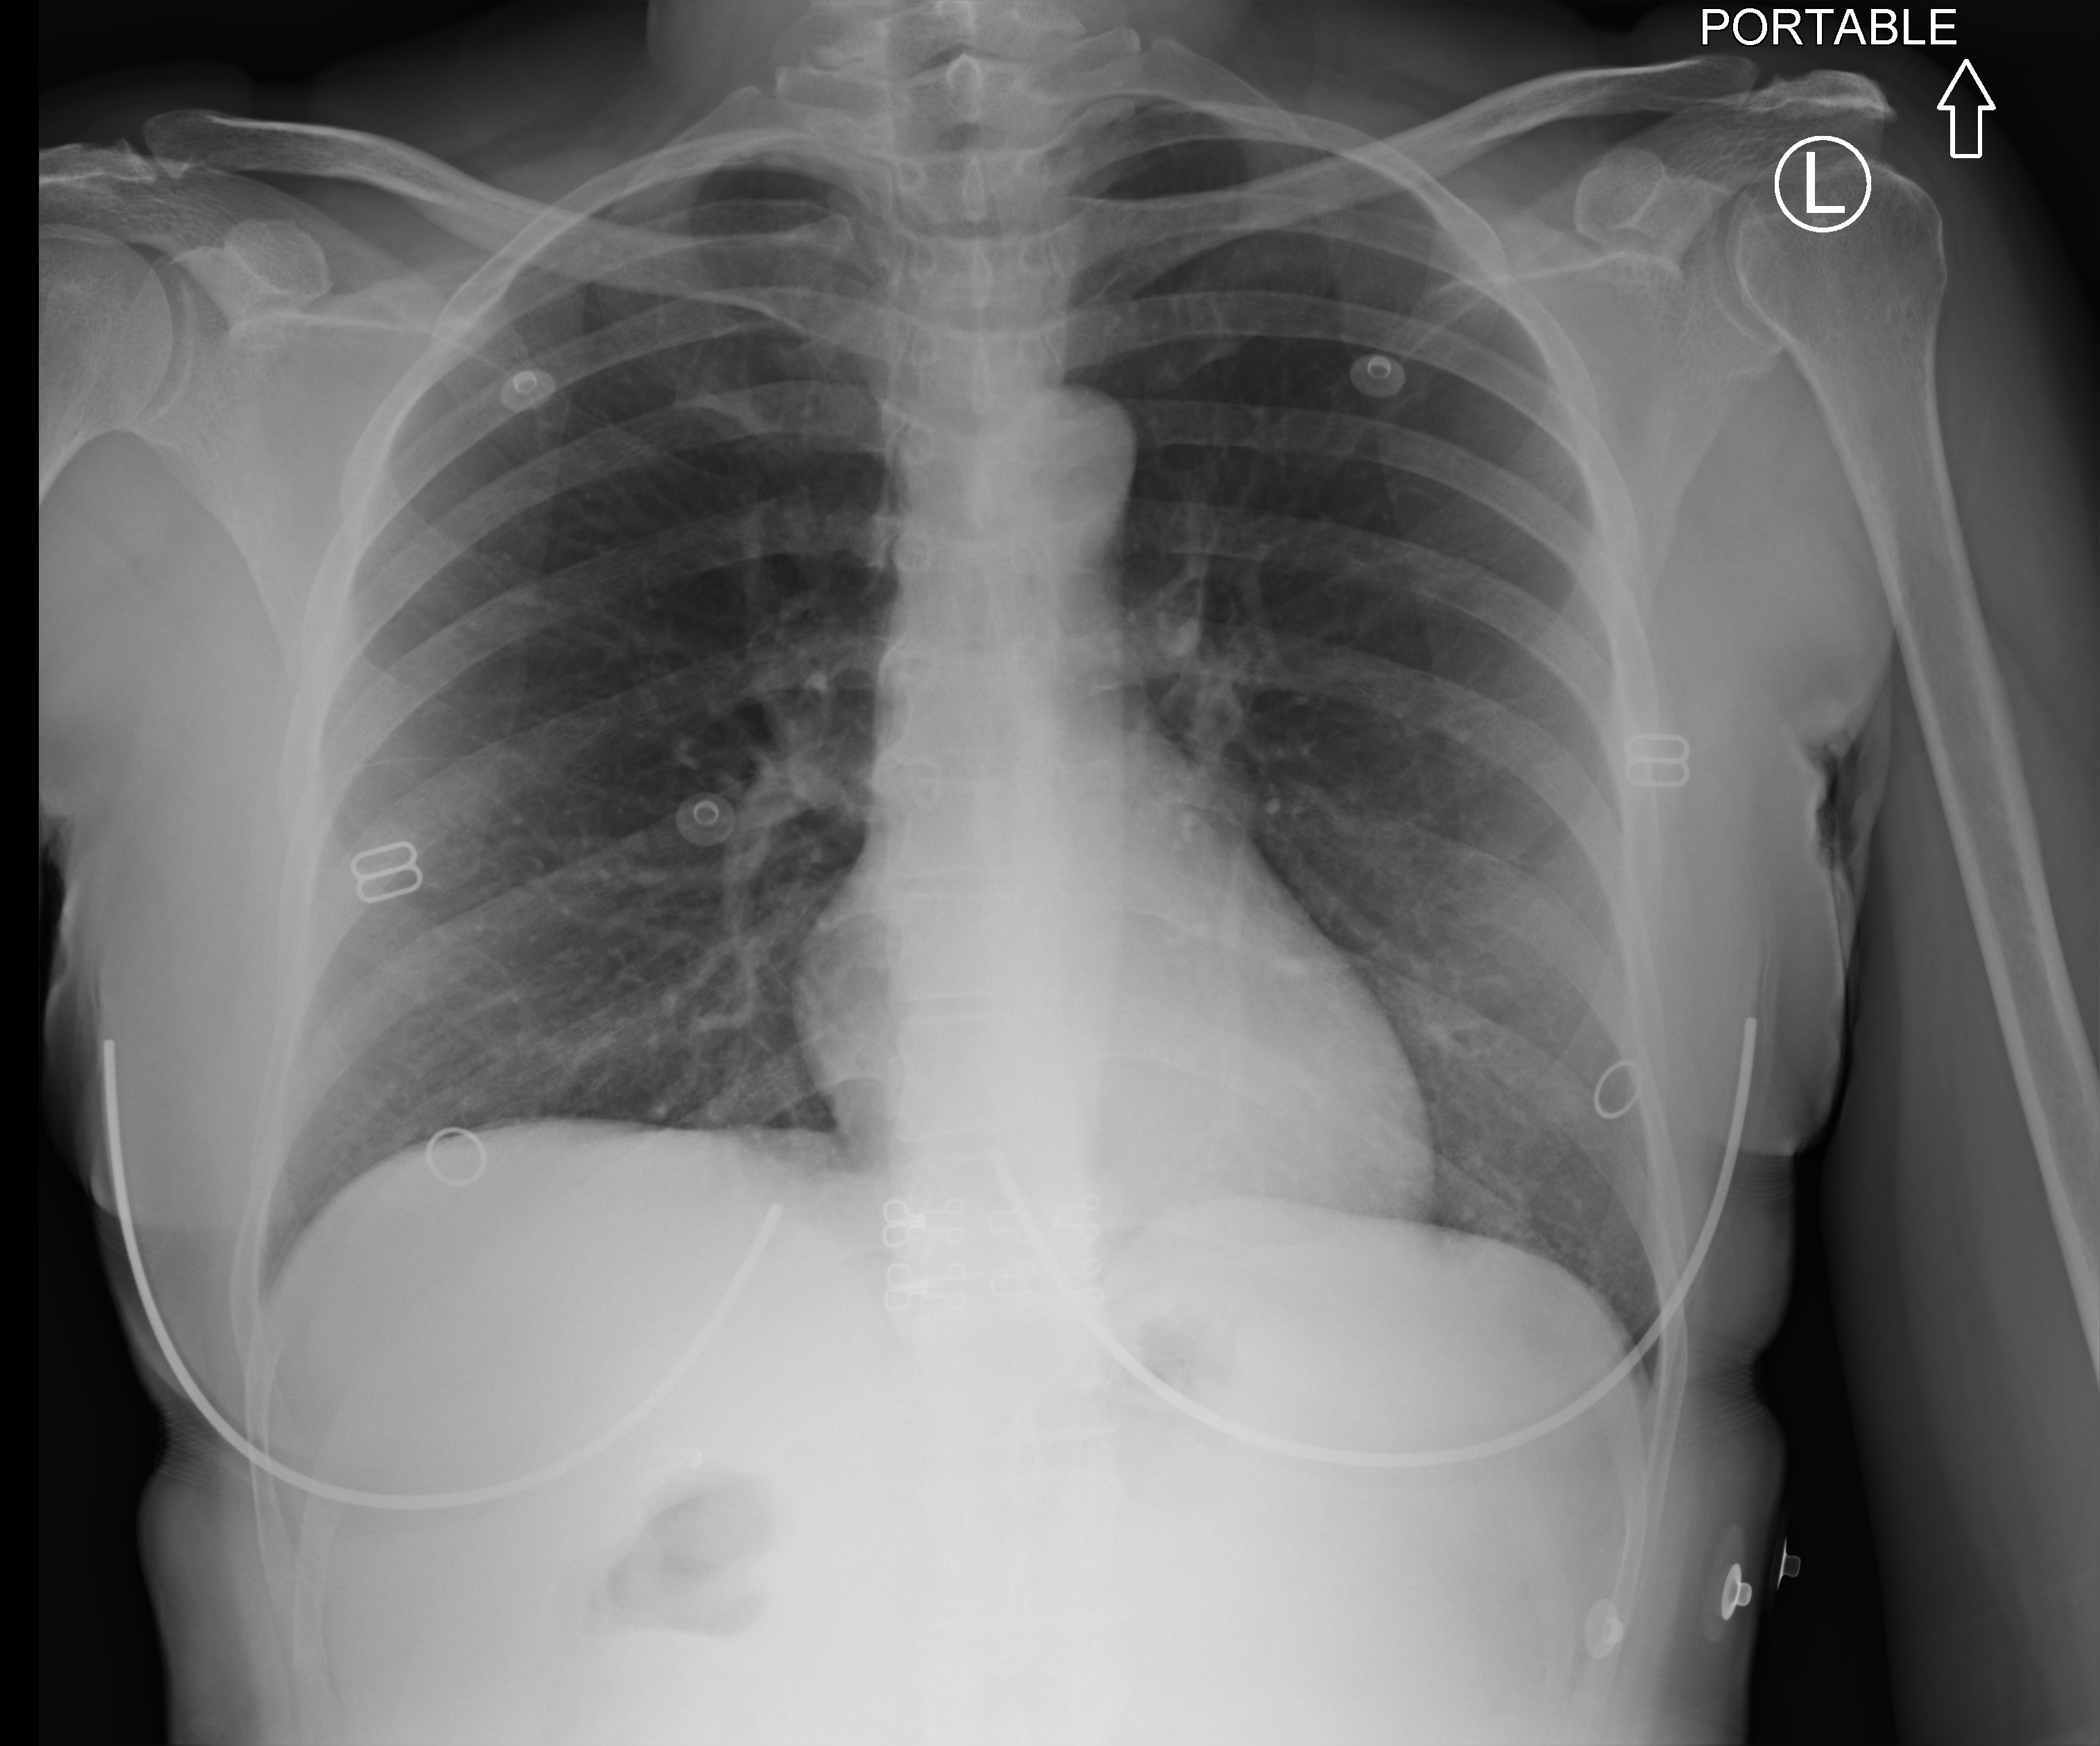
Chest X-ray (portable). Patient hospitalised with COVID-19; female, aged 18–59 years.
Admission-level facts for this patient (not findings on this image; timing relative to this image not recorded):
- chronic kidney disease (admission record): no
- admitted to intensive care during this hospital stay: no
- mechanically ventilated during this hospital stay: no